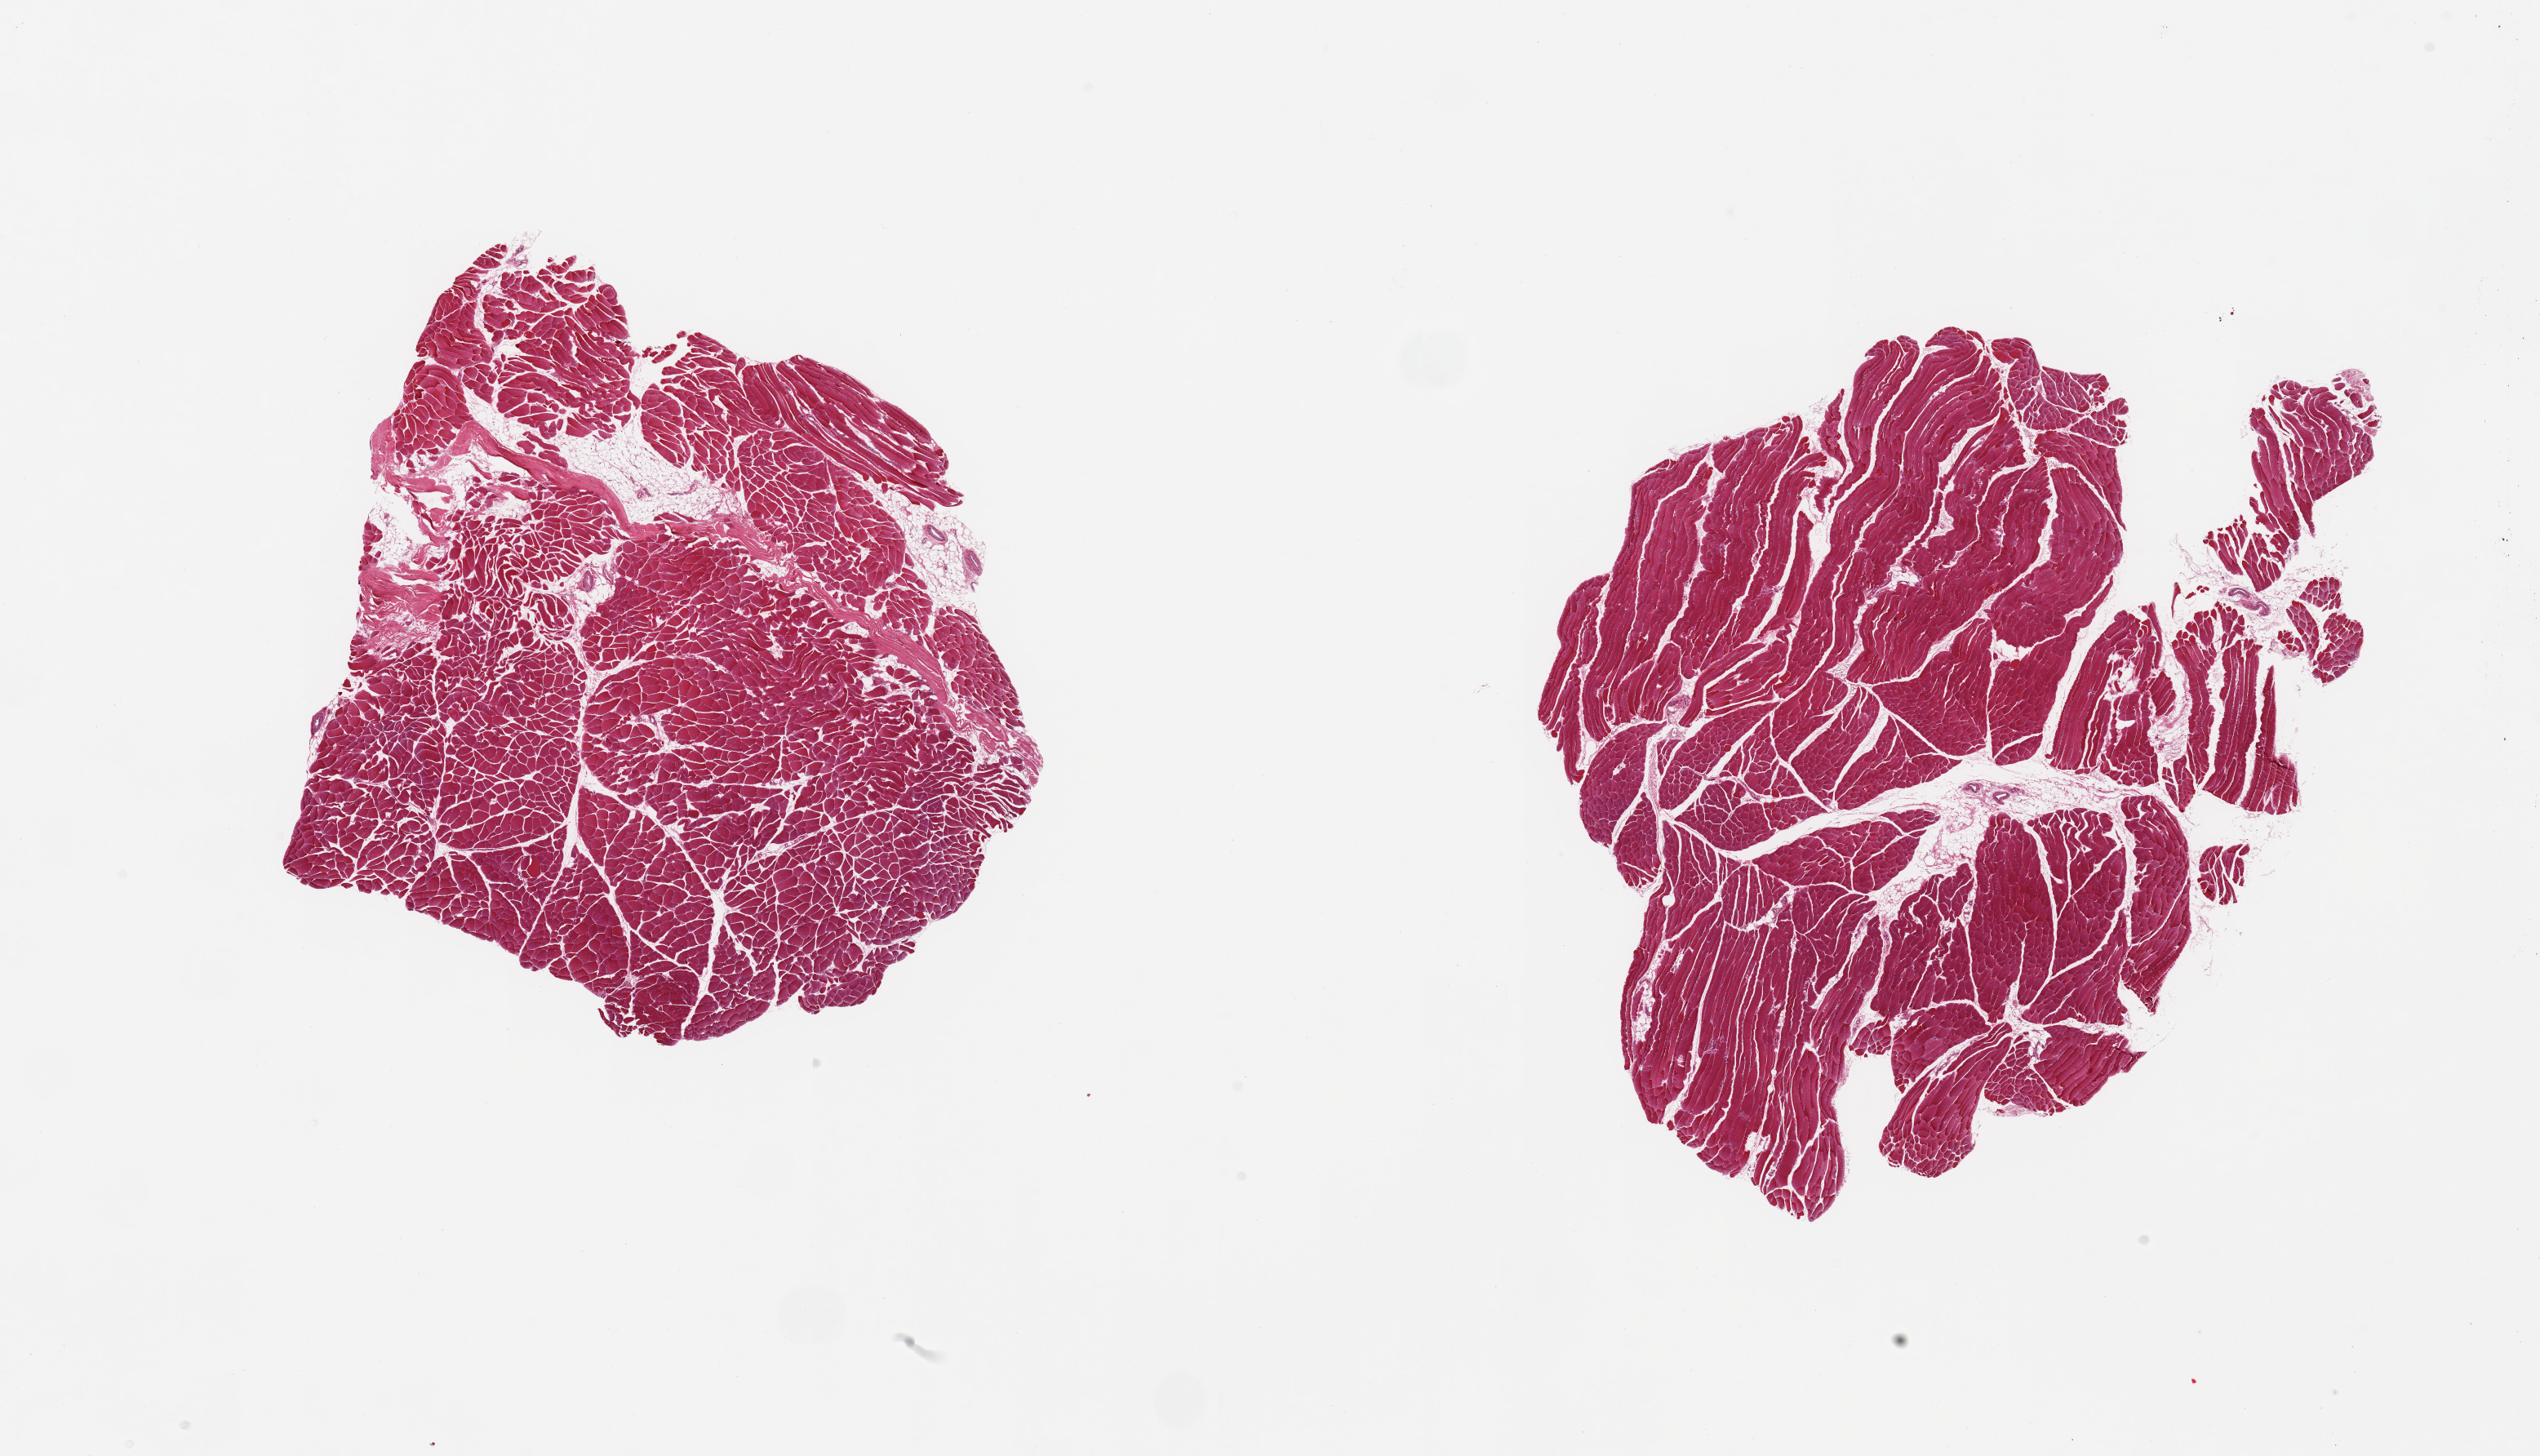
Whole-slide image, haematoxylin and eosin stain, whole scanned area (about 24.6 x 14.1 mm, slide scanned at 20x) shown as a low-resolution overview. PAXgene-fixed paraffin-embedded (PFPE) section. Sampled site (target tissue): skeletal muscle. Donor tissue sample. Male donor.
Pathologist's review note for this sample: 2 pieces; 5% internal fat.